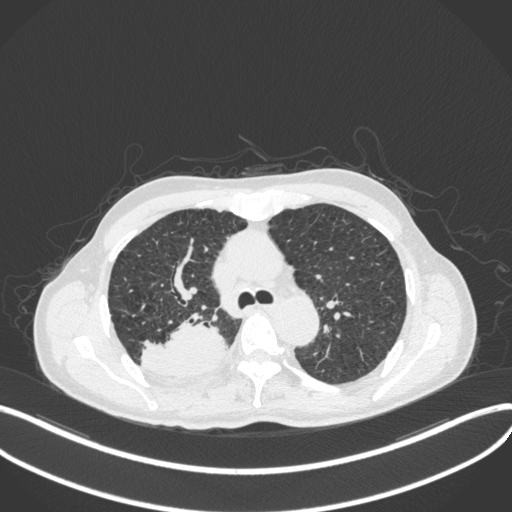
Chest CT, one axial slice; 120 kVp; lung window (W 1500 / L -600 HU); 1 mm slice thickness; 512 × 512 image matrix, field of view 400 × 400 mm. Patient: male, 79 years. Case-level facts recorded for this patient, not image findings: clinical TNM (as recorded): T3 N0 M0.
Annotated regions visible in this slice (bounding box drawn by a radiologist):
- lung tumour (recorded histology: adenocarcinoma): bounding box [x1, y1, x2, y2] px = [140, 315, 226, 379]